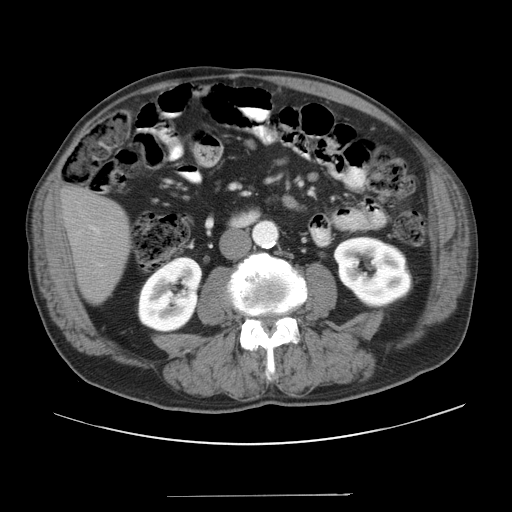
Contrast-enhanced abdominal CT, one axial slice; slice 4 of 41 in the series (ordered by position); reconstruction kernel STANDARD; intravenous contrast given; soft-tissue window (W 400 / L 40 HU); 5 mm slice thickness; 512 × 512 image matrix. Male patient, age 75 years. From the clinical record (not read from this slice): diagnosis: colorectal cancer liver metastases, imaged before liver resection; multiple liver metastases: no.
Structures marked on this image (outlined manually by an expert reader):
- liver: bounding box (x1, y1, x2, y2) in pixels: (62, 189, 130, 302)
- planned liver remnant (the part of the liver to remain after resection): (62, 189, 129, 302)
- portal vein (with intrahepatic branches): (90, 226, 100, 234)